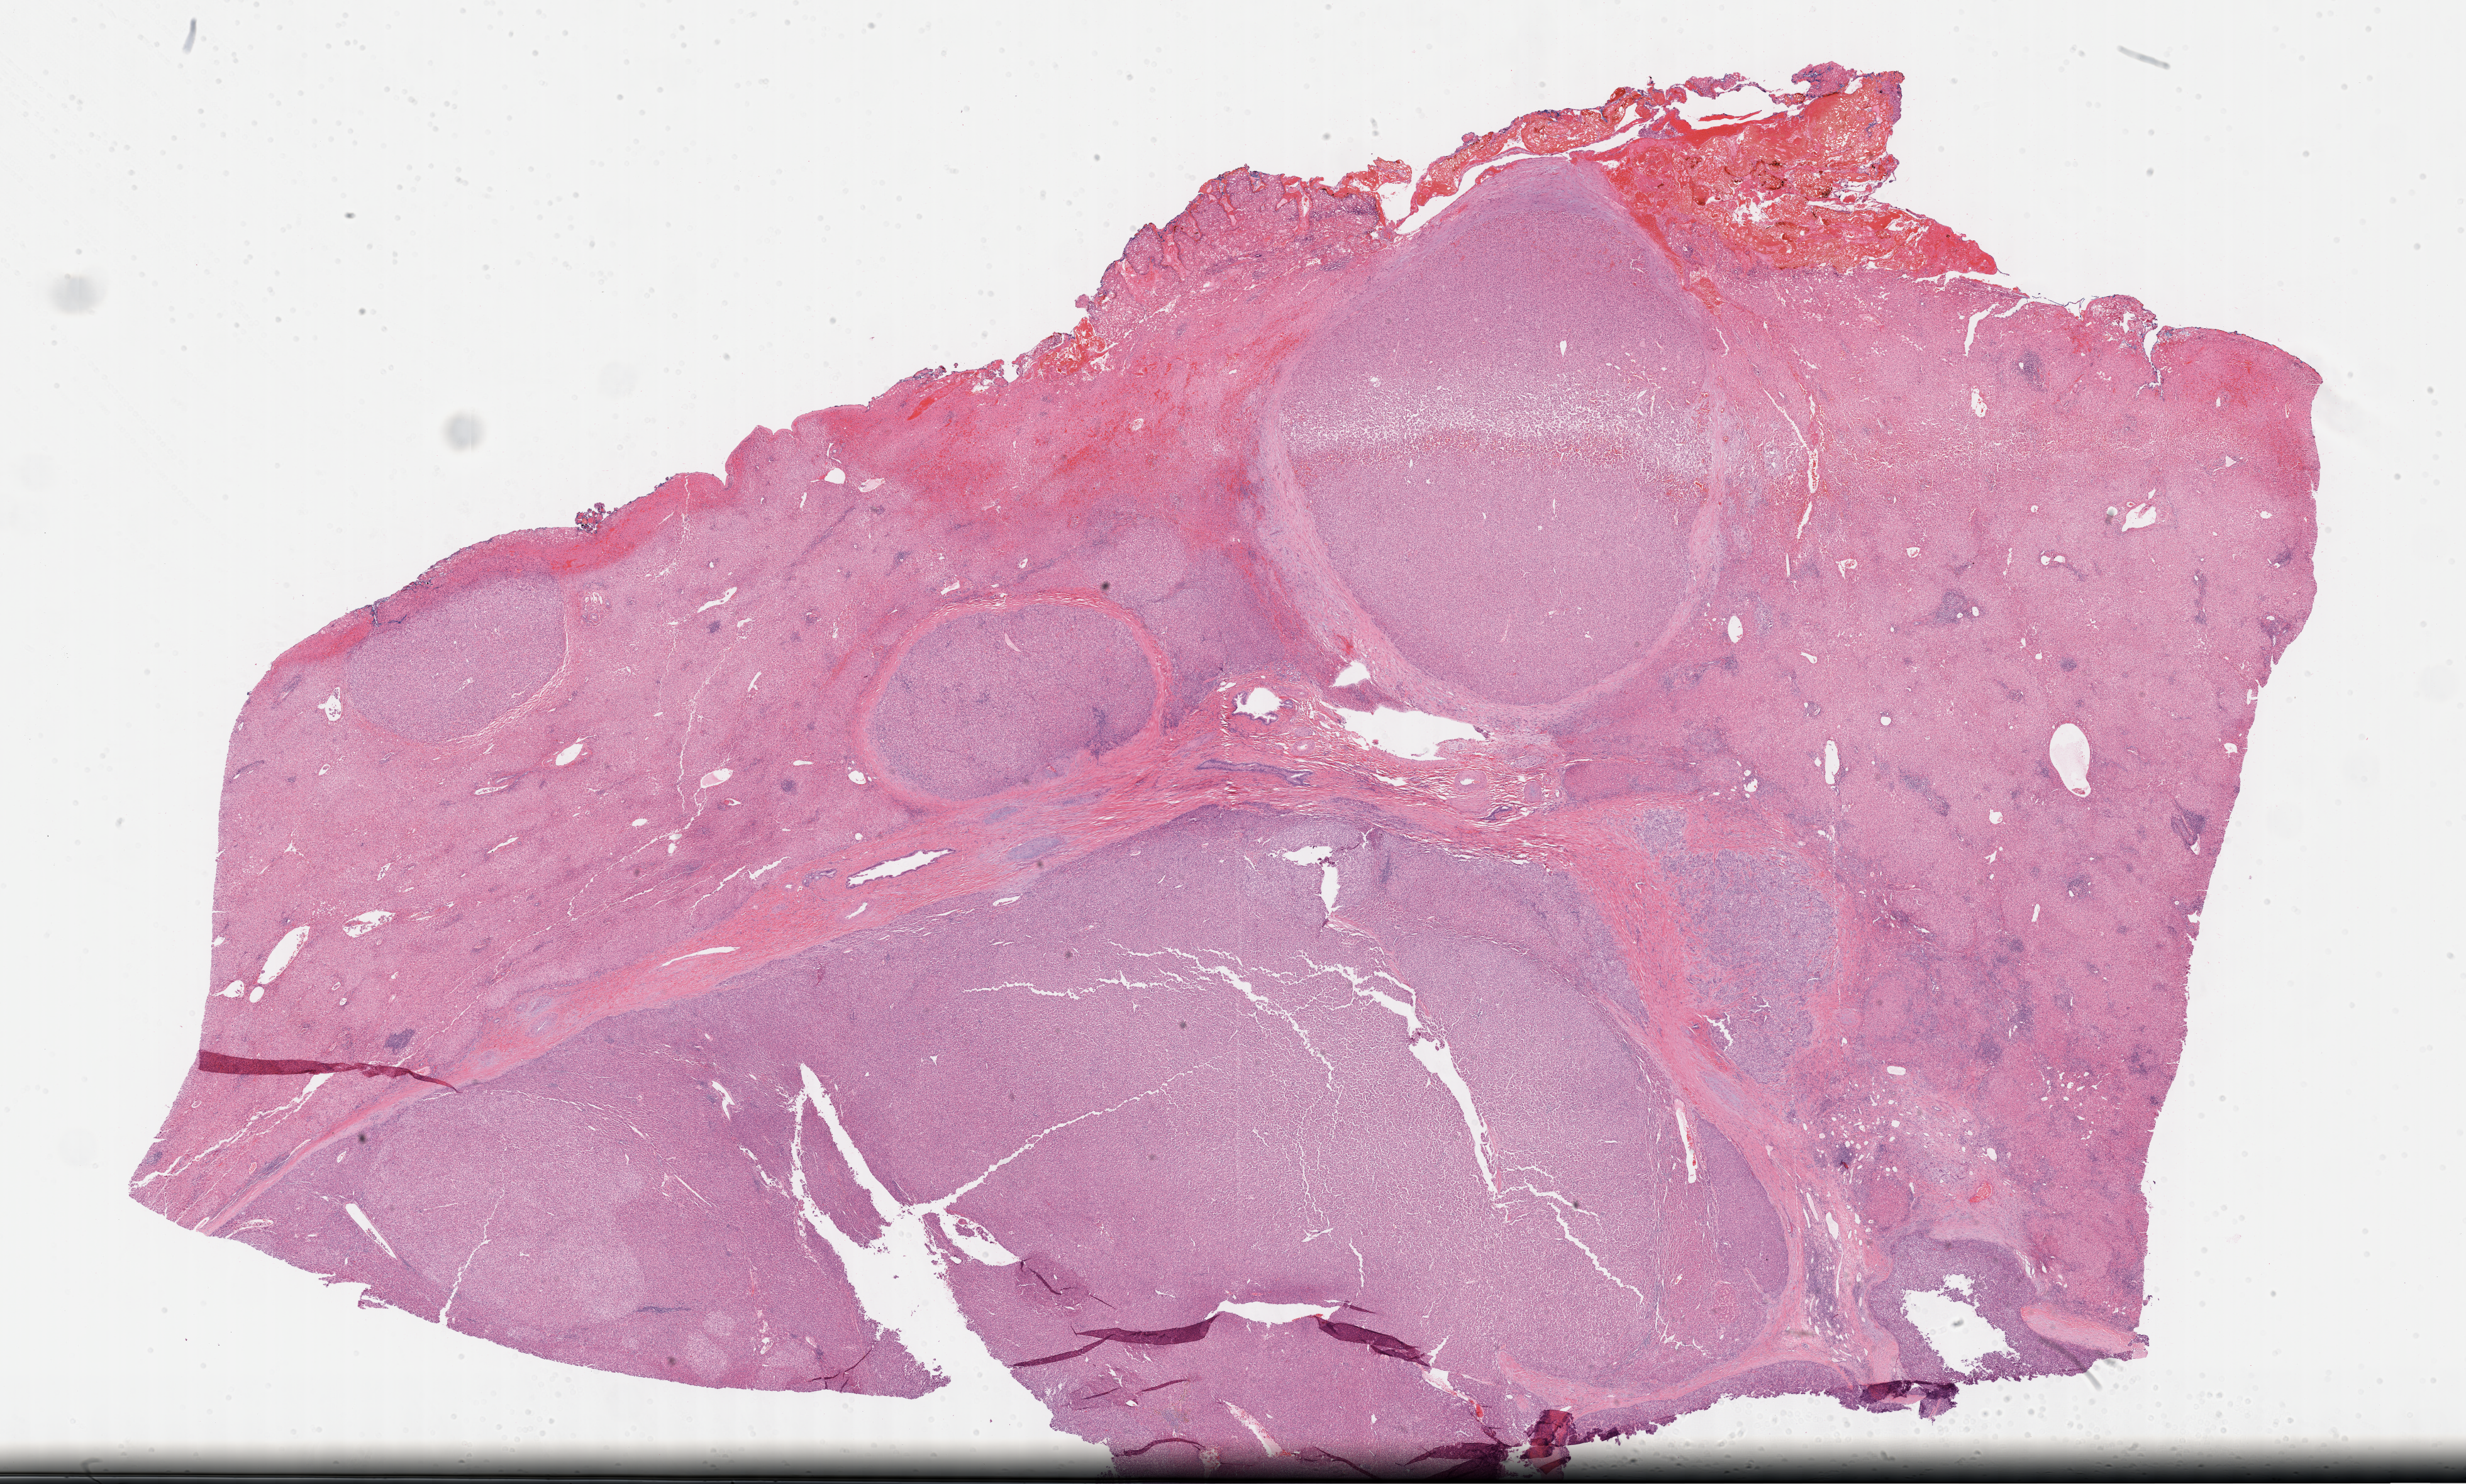
Whole-slide histology image, Hematoxylin and eosin (H&E) stained, shown as a low-resolution overview of the whole scanned area (about 31.7 x 19.1 mm, acquisition: 40x scan); FFPE section; sample: primary tumour, liver. Male, age 60 years at initial diagnosis.
Pathologic diagnosis: Hepatocellular carcinoma, NOS.